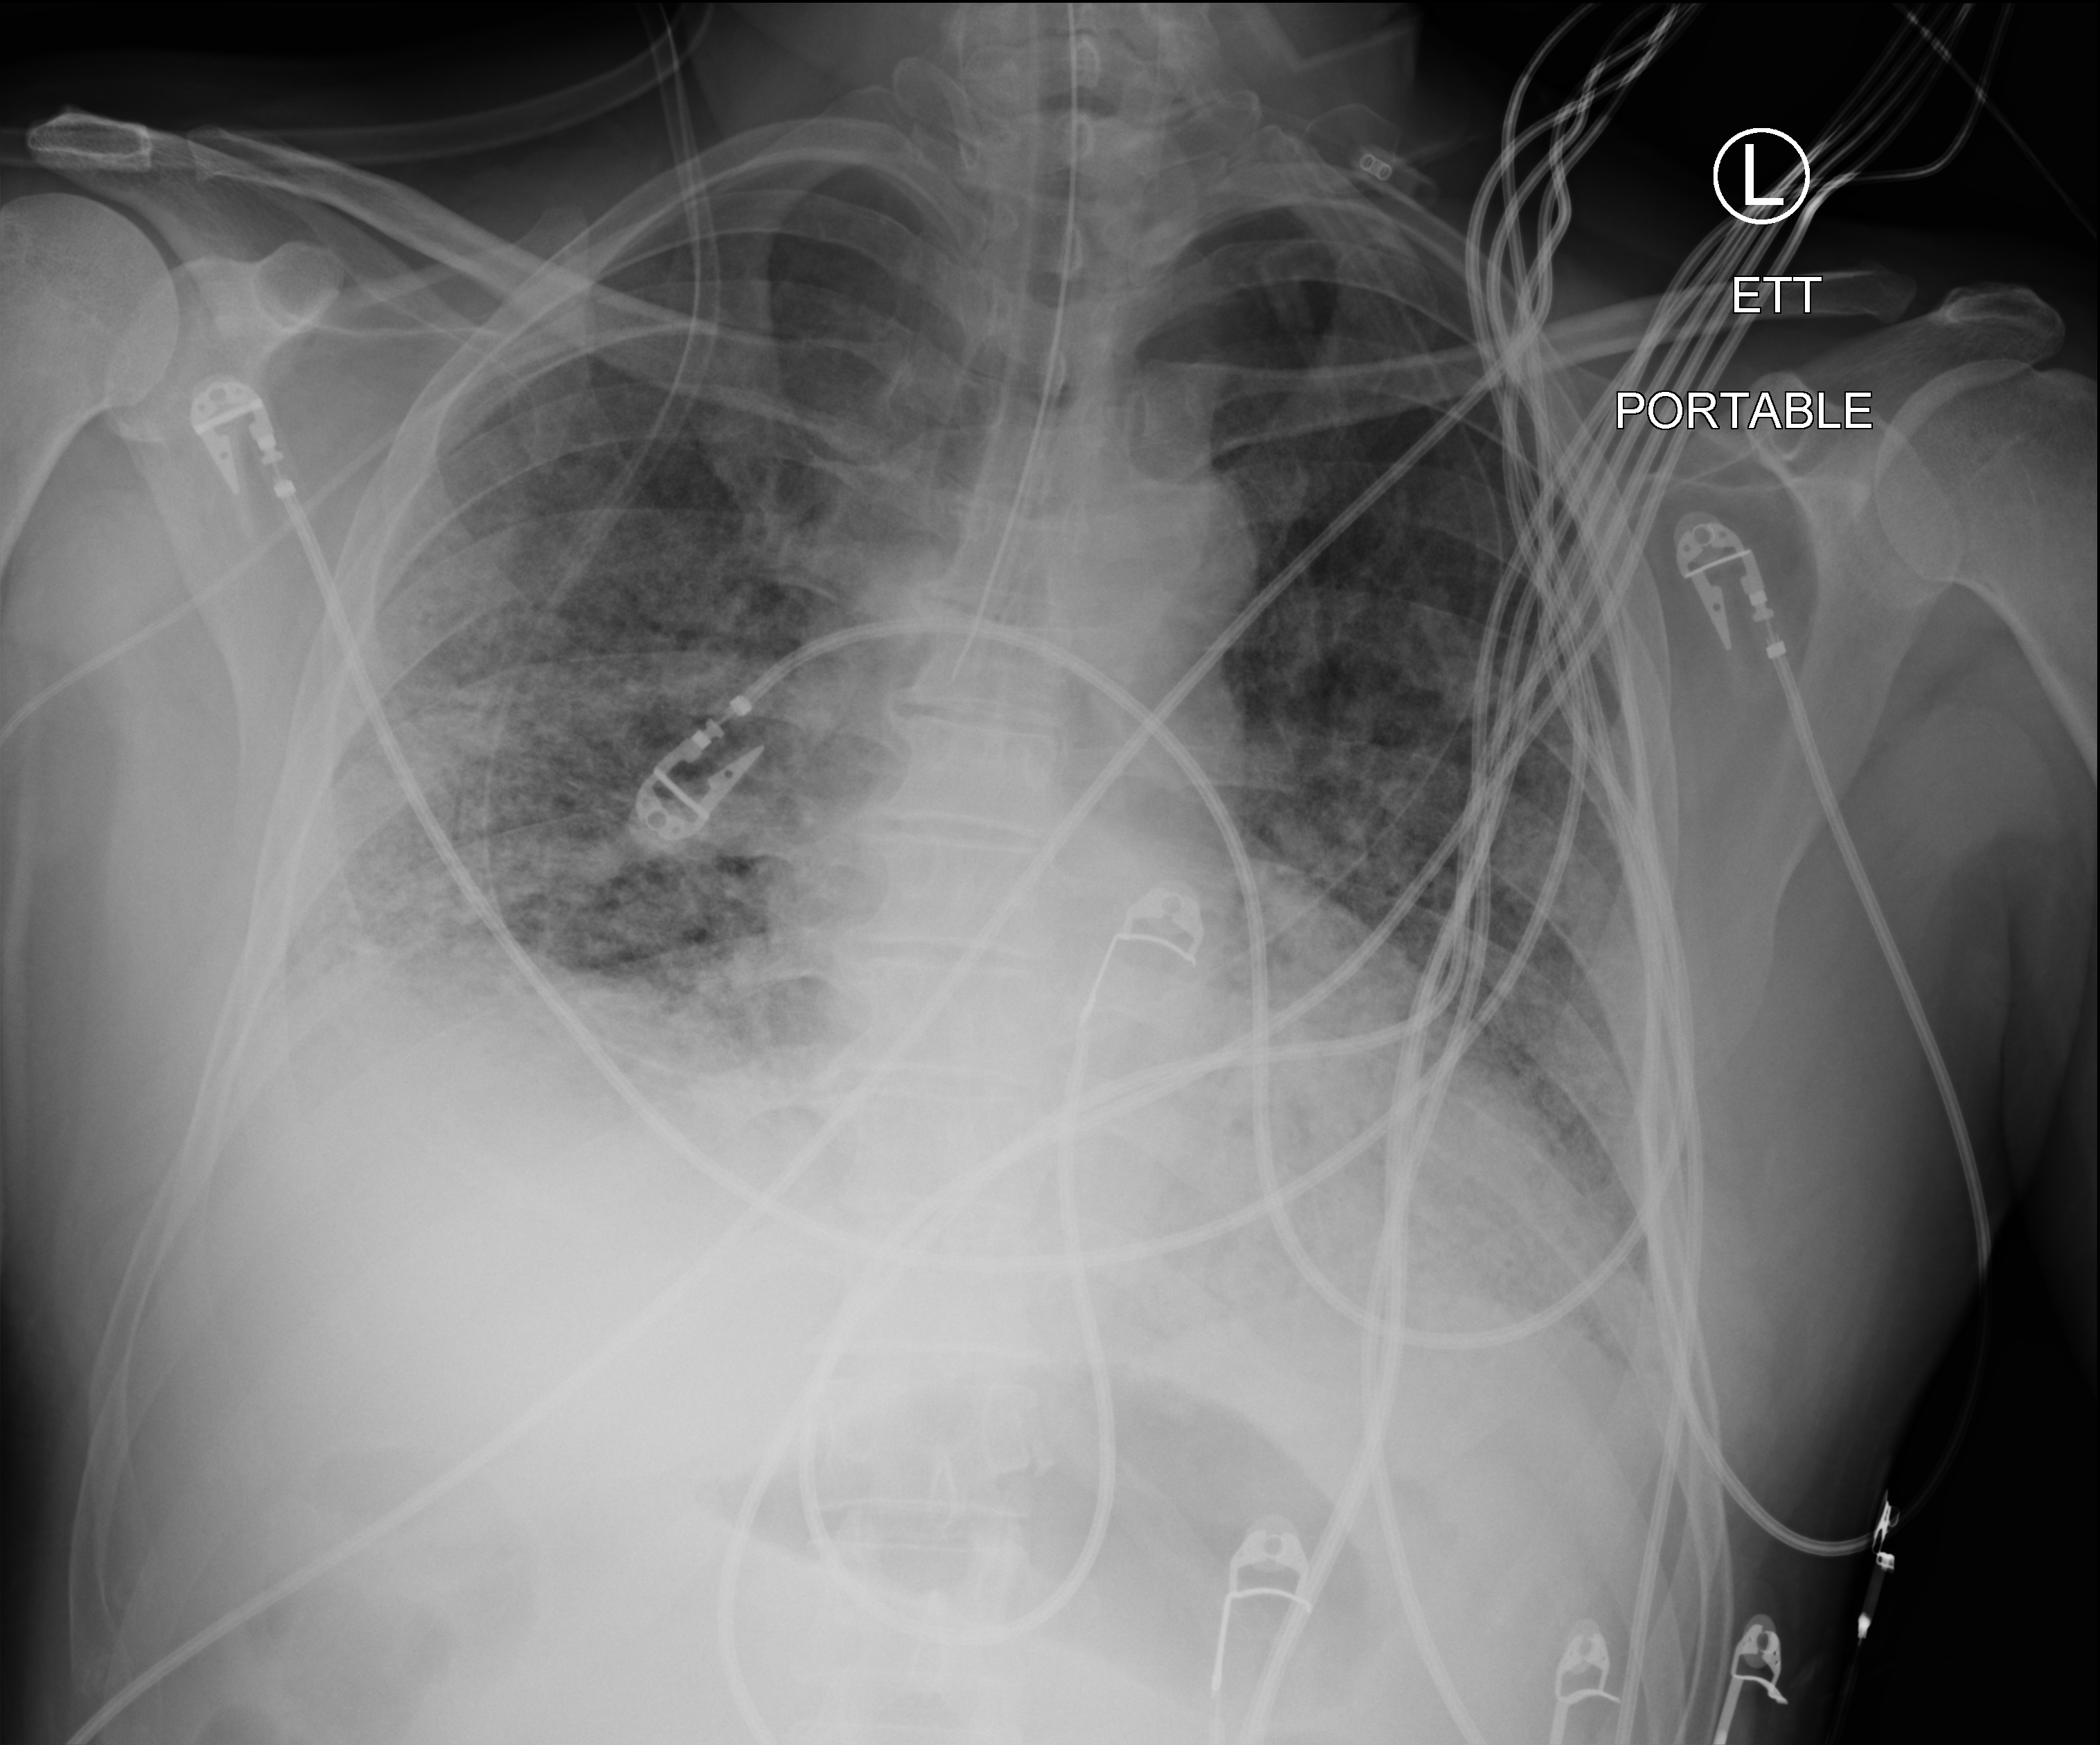
Portable chest radiograph; anteroposterior (AP) projection. Male patient hospitalised with COVID-19, age 18–59 years.
Hospital-stay facts (about this admission, not read from this image; timing relative to this image not recorded): other chronic lung disease (admission record): no; hypertension (admission record): no; admitted to intensive care during this hospital stay: yes.